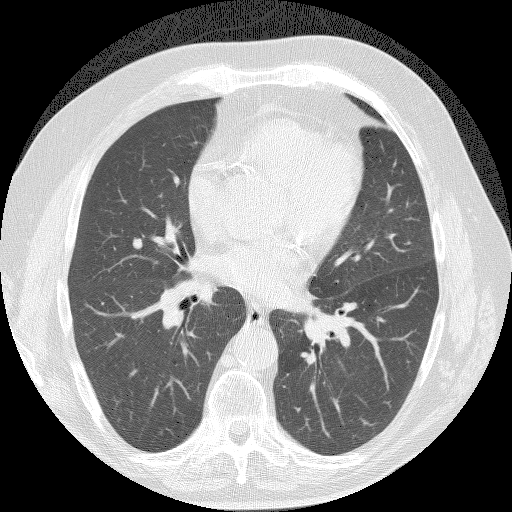
Low-dose screening chest CT, axial slice, baseline screening round, lung window (W 1500 / L -600 HU), lung (sharp) reconstruction kernel (BONE), 140 kVp, slice 81 of 145 in the series. Male participant, aged 61 years at enrolment. Current smoker at enrolment.
Expert reader's lesion annotation, bounding box (x1, y1, x2, y2) in pixels: (110, 226, 155, 263). The screening reader recorded 3 non-calcified nodules or masses ≥4 mm on this exam (right upper lobe, right lower lobe); which of them this box marks is not recorded. Lung cancer was diagnosed 491 days after this screen: bronchiolo-alveolar adenocarcinoma, NOS, right middle lobe, well differentiated (G1), stage IA (AJCC 6th edition), 15 mm at pathology.